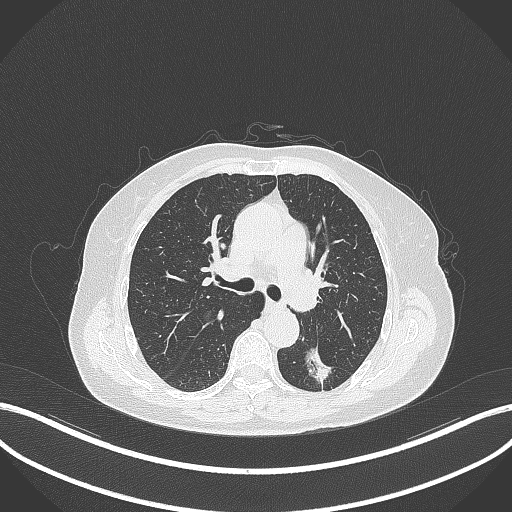
Chest CT, one axial slice. Slice 188 of 352 in the series (ordered by position). Reconstruction kernel B70f. 120 kVp. Lung window (W 1500 / L -600 HU). 1 mm slice thickness. 512 × 512 image matrix, field of view 400 × 400 mm. Patient: female, 70 years. From the clinical record (not read from this slice): clinical TNM (as recorded): T1c N0 M0.
Annotated regions visible in this slice (bounding box drawn by a radiologist):
- lung tumour (recorded histology: adenocarcinoma): bounding box [x1, y1, x2, y2] px = [300, 338, 336, 386]